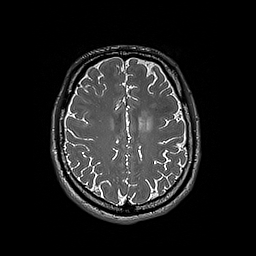
Brain MRI from a brain-tumour surgery series, one axial slice; position 65 of 192 along the scan axis; 256 × 256 image matrix, field of view 250 × 250 mm. From the clinical record (not read from this slice): histopathology: Oligodendroglioma; WHO grade: 3; IDH mutation: yes.
Structures marked on this image (expert manual segmentation):
- tumour: bounding box <138,118,154,130> (left, top, right, bottom; pixels)